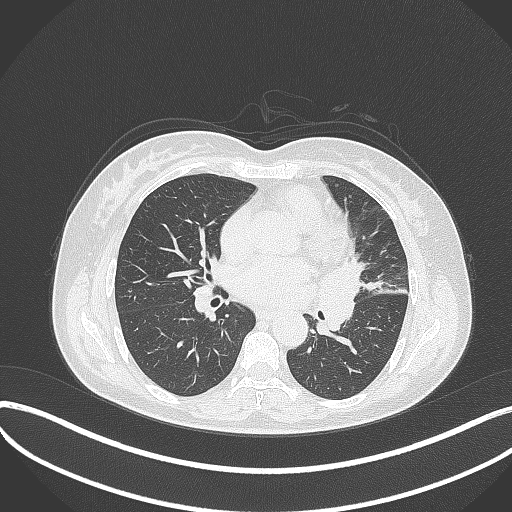
Chest CT, one axial slice. Slice 176 of 373 in the series (ordered by position). Reconstruction kernel B70f. 120 kVp. Lung window (W 1500 / L -600 HU). 1 mm slice thickness. 512 × 512 image matrix, field of view 400 × 400 mm. Patient: female, 54 years. From the clinical record (not read from this slice): clinical TNM (as recorded): T2a N1 M0.
Outlined on this slice (rectangle marked by the reading radiologist):
- lung tumour (recorded histology: small cell carcinoma): bounding box [x1, y1, x2, y2] px = [316, 253, 368, 332]